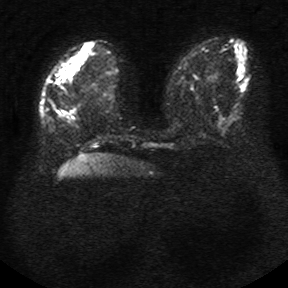
Breast MRI, one axial slice. Position 10 of 34 along the scan axis. Diffusion-weighted series; image 2 of 4 stored at this slice position (different b-values; order by instance number). 1.5 T. 5 mm slice thickness. 288 × 288 image matrix, field of view 340 × 340 mm. Female patient.
Structures marked on this image (outlined manually by an expert reader):
- tumour on diffusion-weighted imaging: bounding box <56,42,94,83> (left, top, right, bottom; pixels)